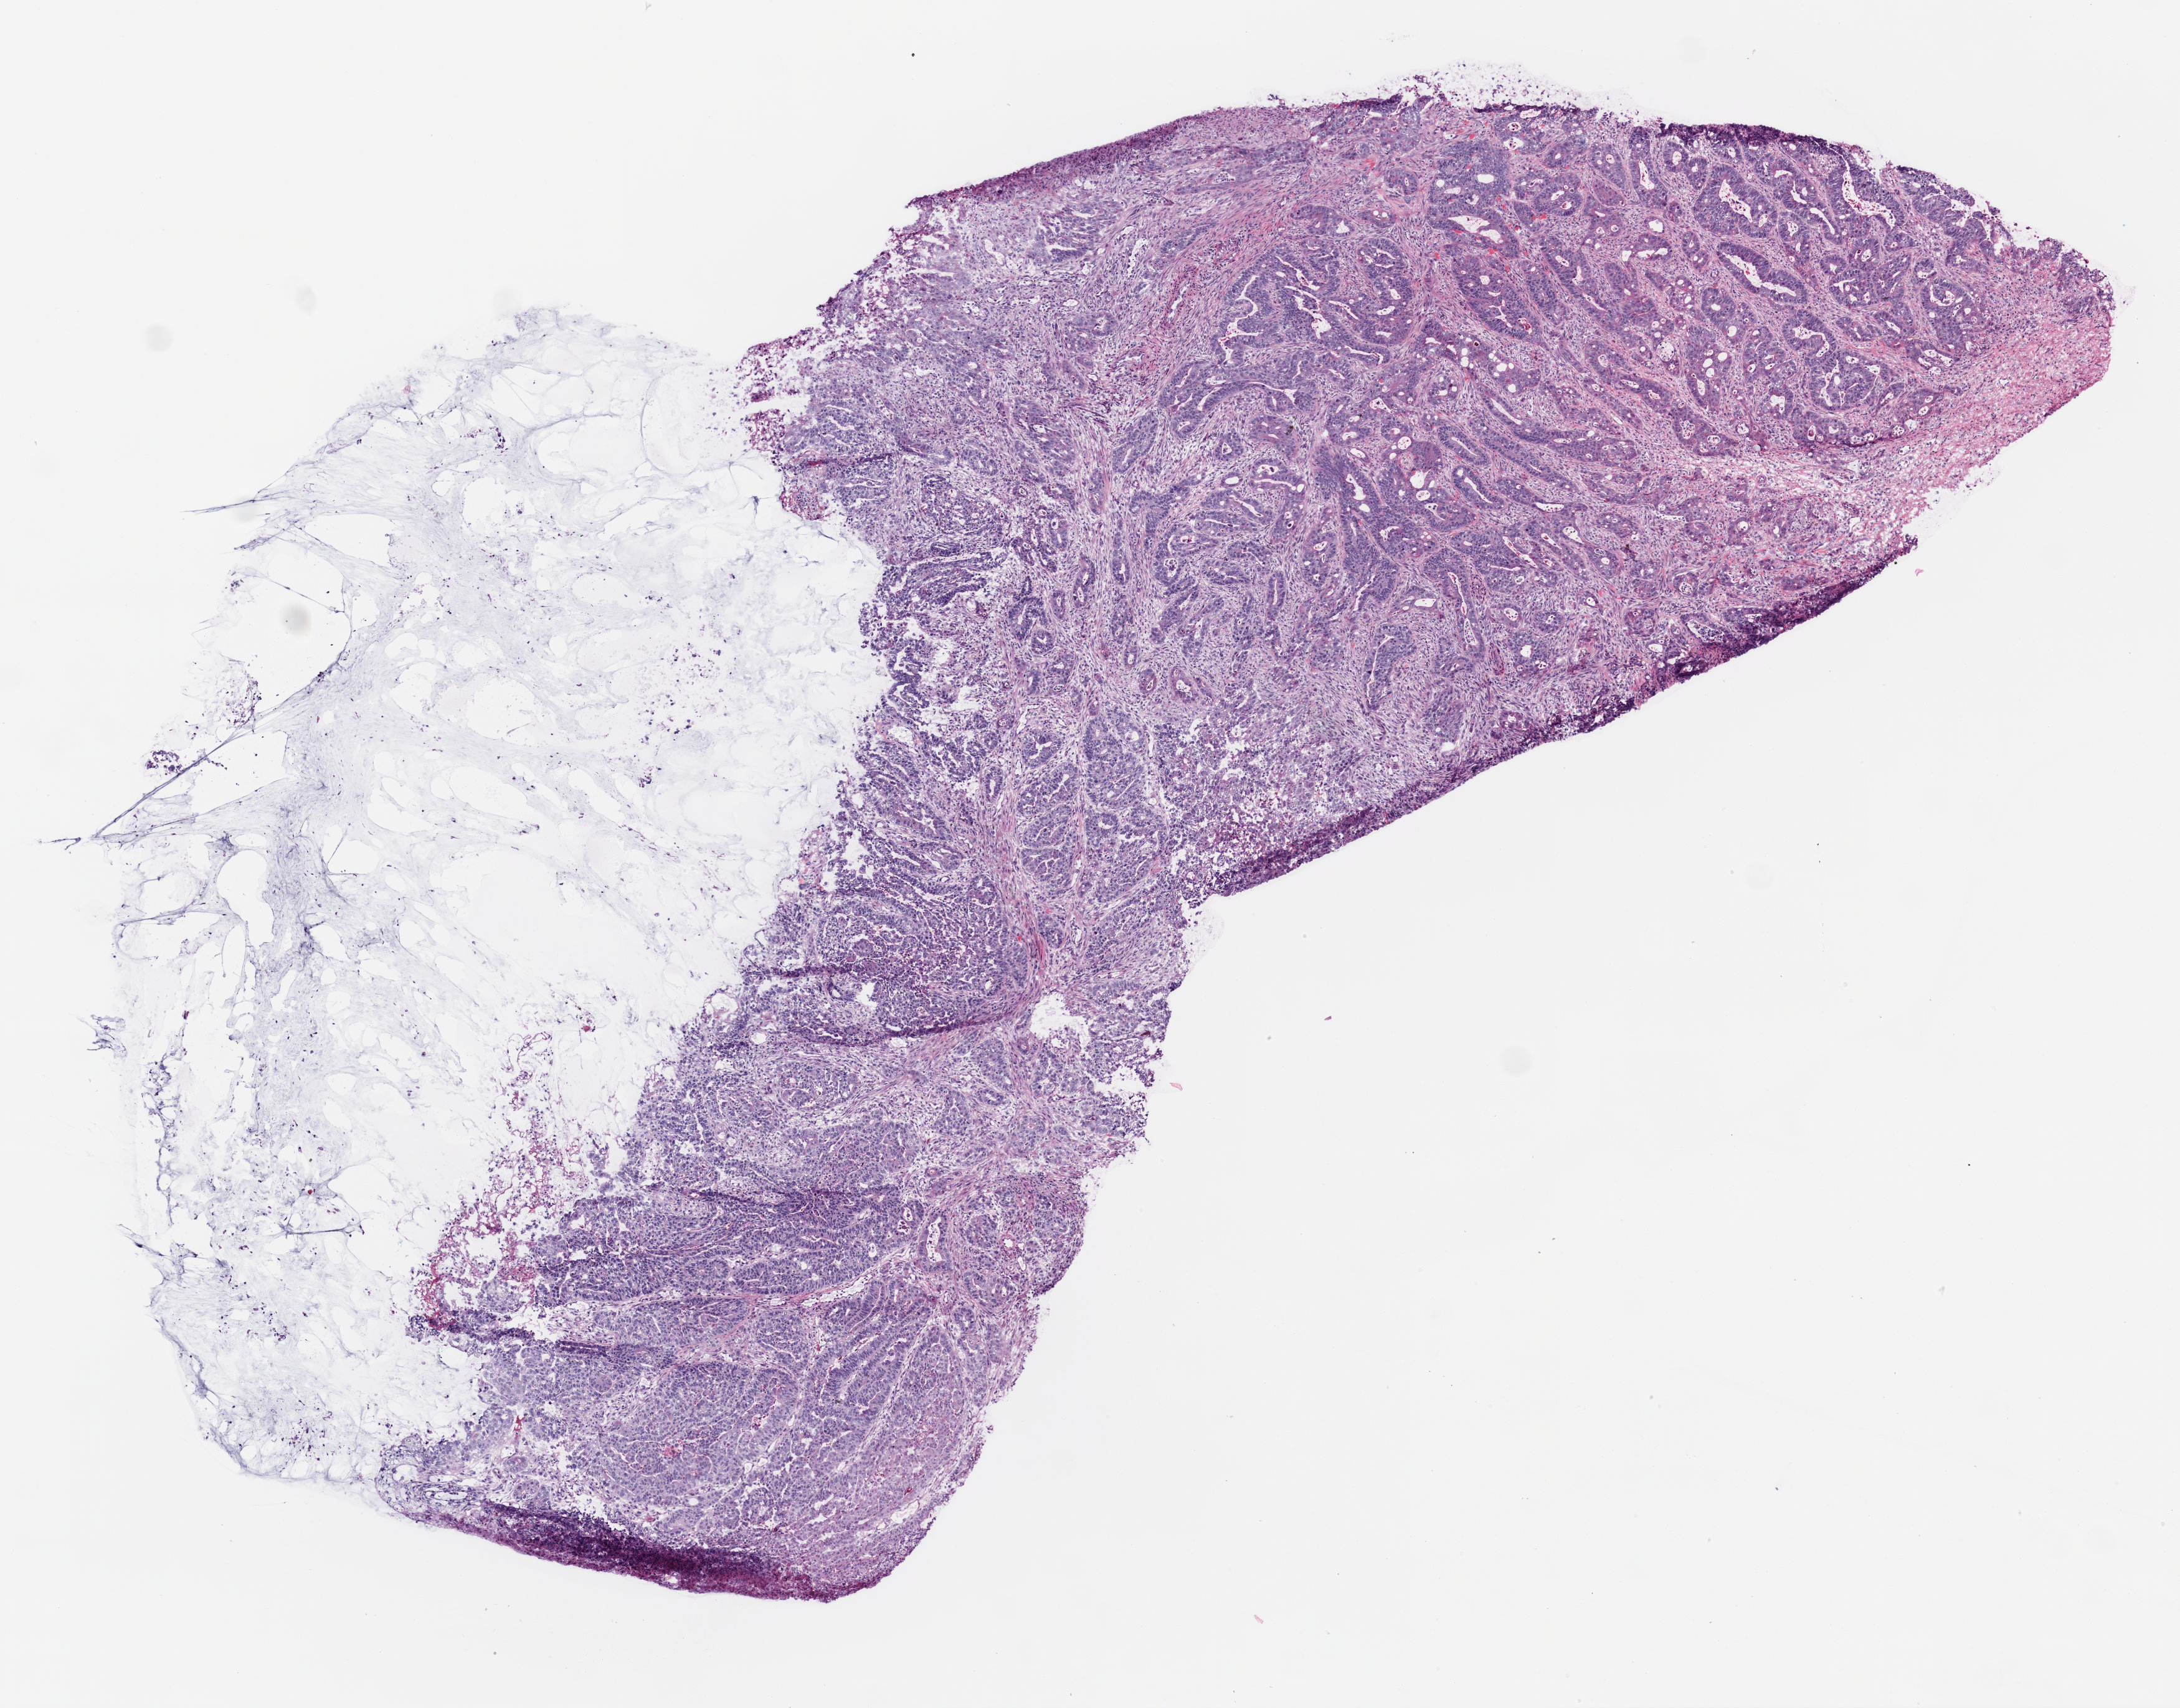
Whole-slide histology image, H&E-stained — a low-resolution overview of the entire scanned area, about 7.0 x 5.5 mm (slide scanned at 20x). Frozen section. Primary tumour sample from the rectum. Male, age 64 years at initial diagnosis. Pathologist review of this section (percent, as recorded): tumour cells 80%, tumour nuclei 80%, normal cells 0%, stromal cells 15%, necrosis 5%.
- lymph nodes positive (case pathology): 7 of 40 examined
- AJCC pathologic stage: IV (6th edition)
- diagnosis: Adenocarcinoma, NOS